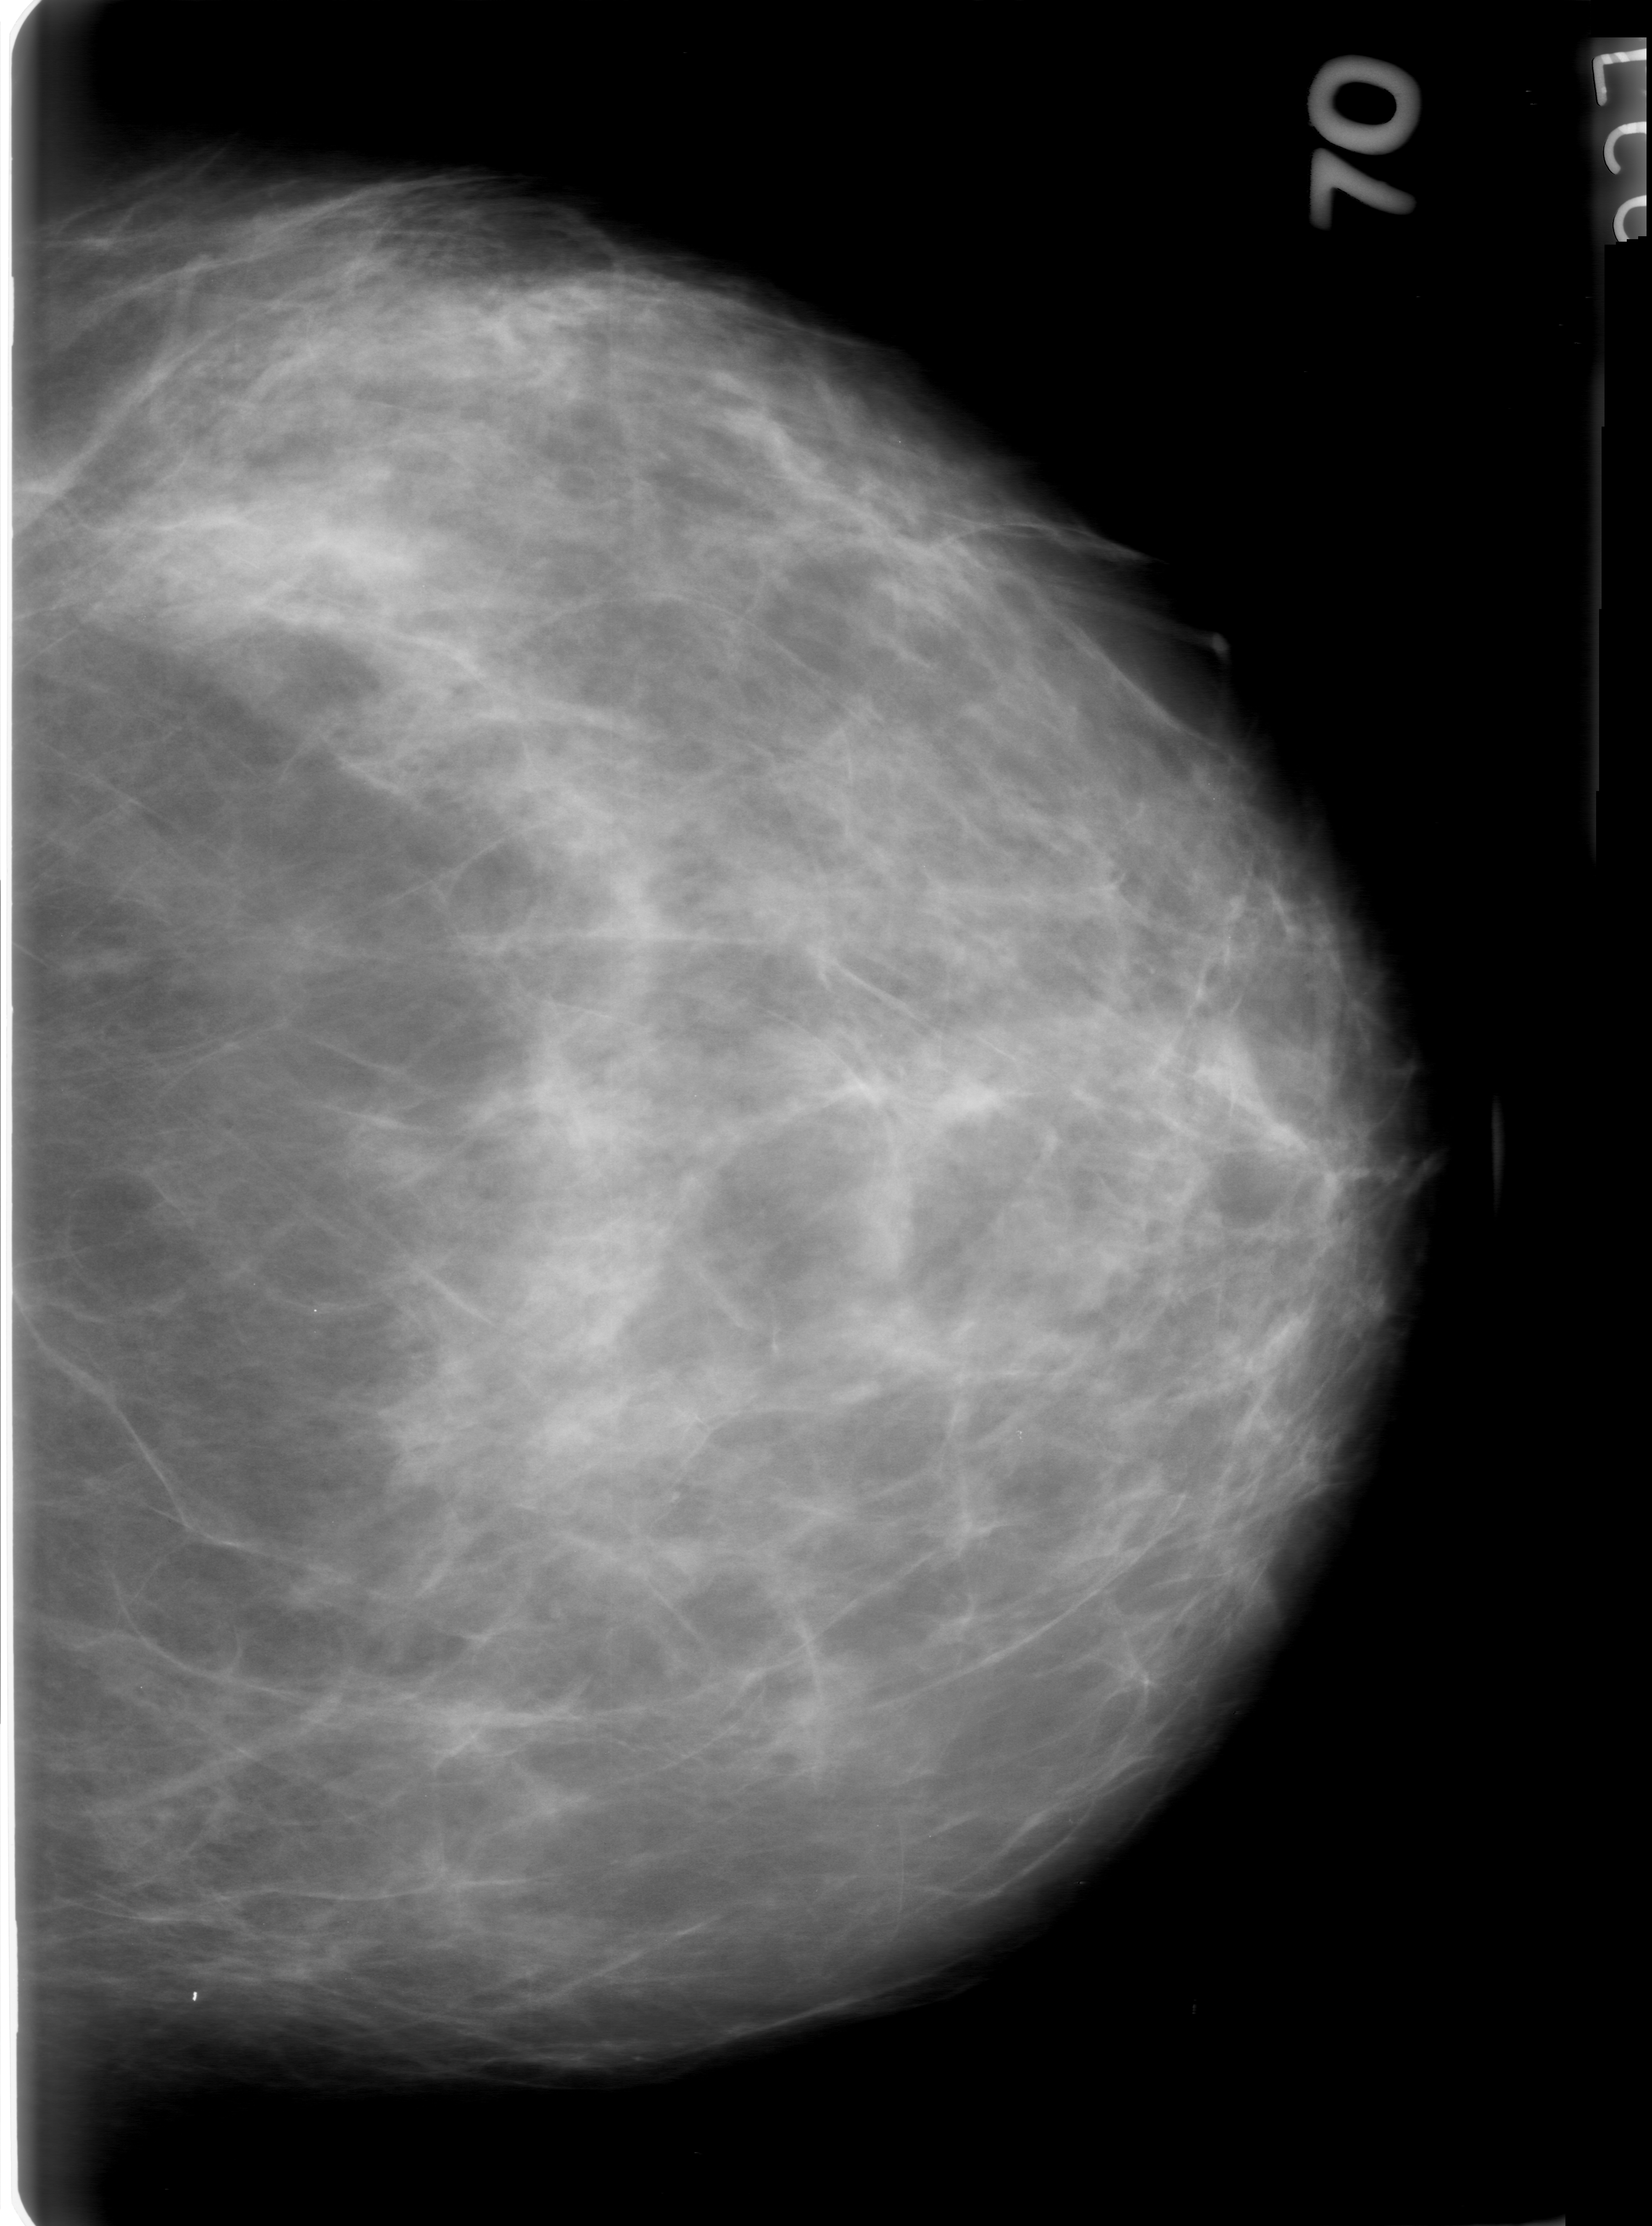
Digitized screen-film mammogram; left breast; craniocaudal (CC) view; breast composition: heterogeneously dense (BI-RADS density category 3 of 4); 1652 × 2226 image matrix.
Expert-marked regions of interest on this film, with their recorded descriptors:
- mass, shape oval, margins obscured; BI-RADS assessment category 0; subtlety rating 4 on a 1 (subtle) to 5 (obvious) scale; pathology result (as recorded, not read from the image): benign: bounding box [x1, y1, x2, y2] px = [828, 1168, 934, 1291]